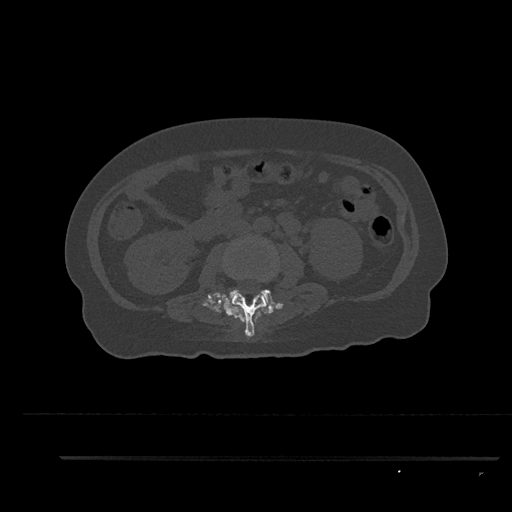
CT including the spine, one axial slice. Slice 126 of 797 in the series (ordered by position). 120 kVp. Bone window (W 1800 / L 400 HU). 0.5 mm slice thickness. 512 × 512 image matrix. Patient: female, 44 years. From the clinical record (not read from this slice): primary cancer: renal; vertebrae with lytic lesions (as recorded): L1.
Structures marked on this image (semi-automatic segmentation, software-assisted and operator-edited):
- L2 vertebra: bounding box <226,292,268,337> (left, top, right, bottom; pixels)
- L3 vertebra: <223,240,276,306>